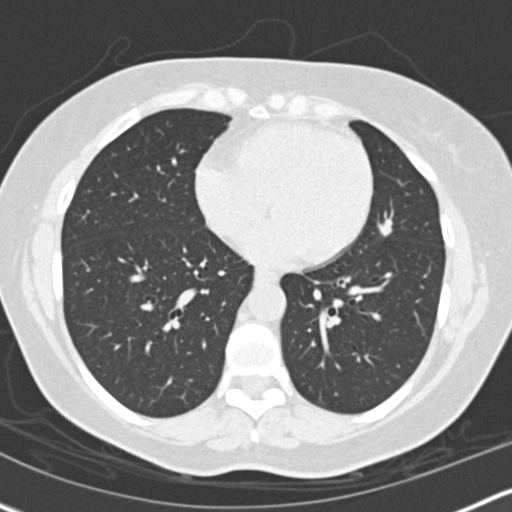
Axial slice from a low-dose chest CT screening exam. Second screening round (one year after baseline). Lung window (W 1500 / L -600 HU). 2 mm slice thickness. Slice 92 of 158 in the series. Female, age 56 years at enrolment. Former smoker at enrolment.
- Expert reader's lesion annotation, box from (x=358, y=202) to (x=408, y=251) px.
- Screening reader's record for this exam (one nodule recorded; not confirmed to be the boxed lesion): non-calcified nodule or mass ≥4 mm, lingula, 10 × 8 mm, smooth margins, soft tissue attenuation, pre-existing on the prior screen: yes; interval growth: yes.
- Lung cancer was diagnosed 506 days after this screen: adenocarcinoma, NOS, left upper lobe, poorly differentiated (G3), stage IIIA (AJCC 6th edition), 15 mm at pathology.